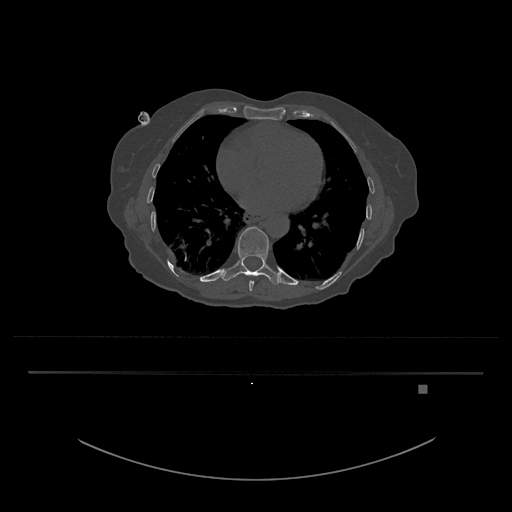
CT including the spine, one axial slice; position 725 of 797 along the scan axis; 120 kVp; bone window (W 1800 / L 400 HU); 0.5 mm slice thickness; 512 × 512 image matrix, field of view 500 × 500 mm. Female patient, age 57 years. From the clinical record (not read from this slice): primary cancer: cervical.
Outlined on this slice (semi-automatic segmentation, software-assisted and operator-edited):
- T10 vertebra: bounding box (x1, y1, x2, y2) in pixels: (222, 226, 284, 285)
- T9 vertebra: (249, 281, 255, 291)